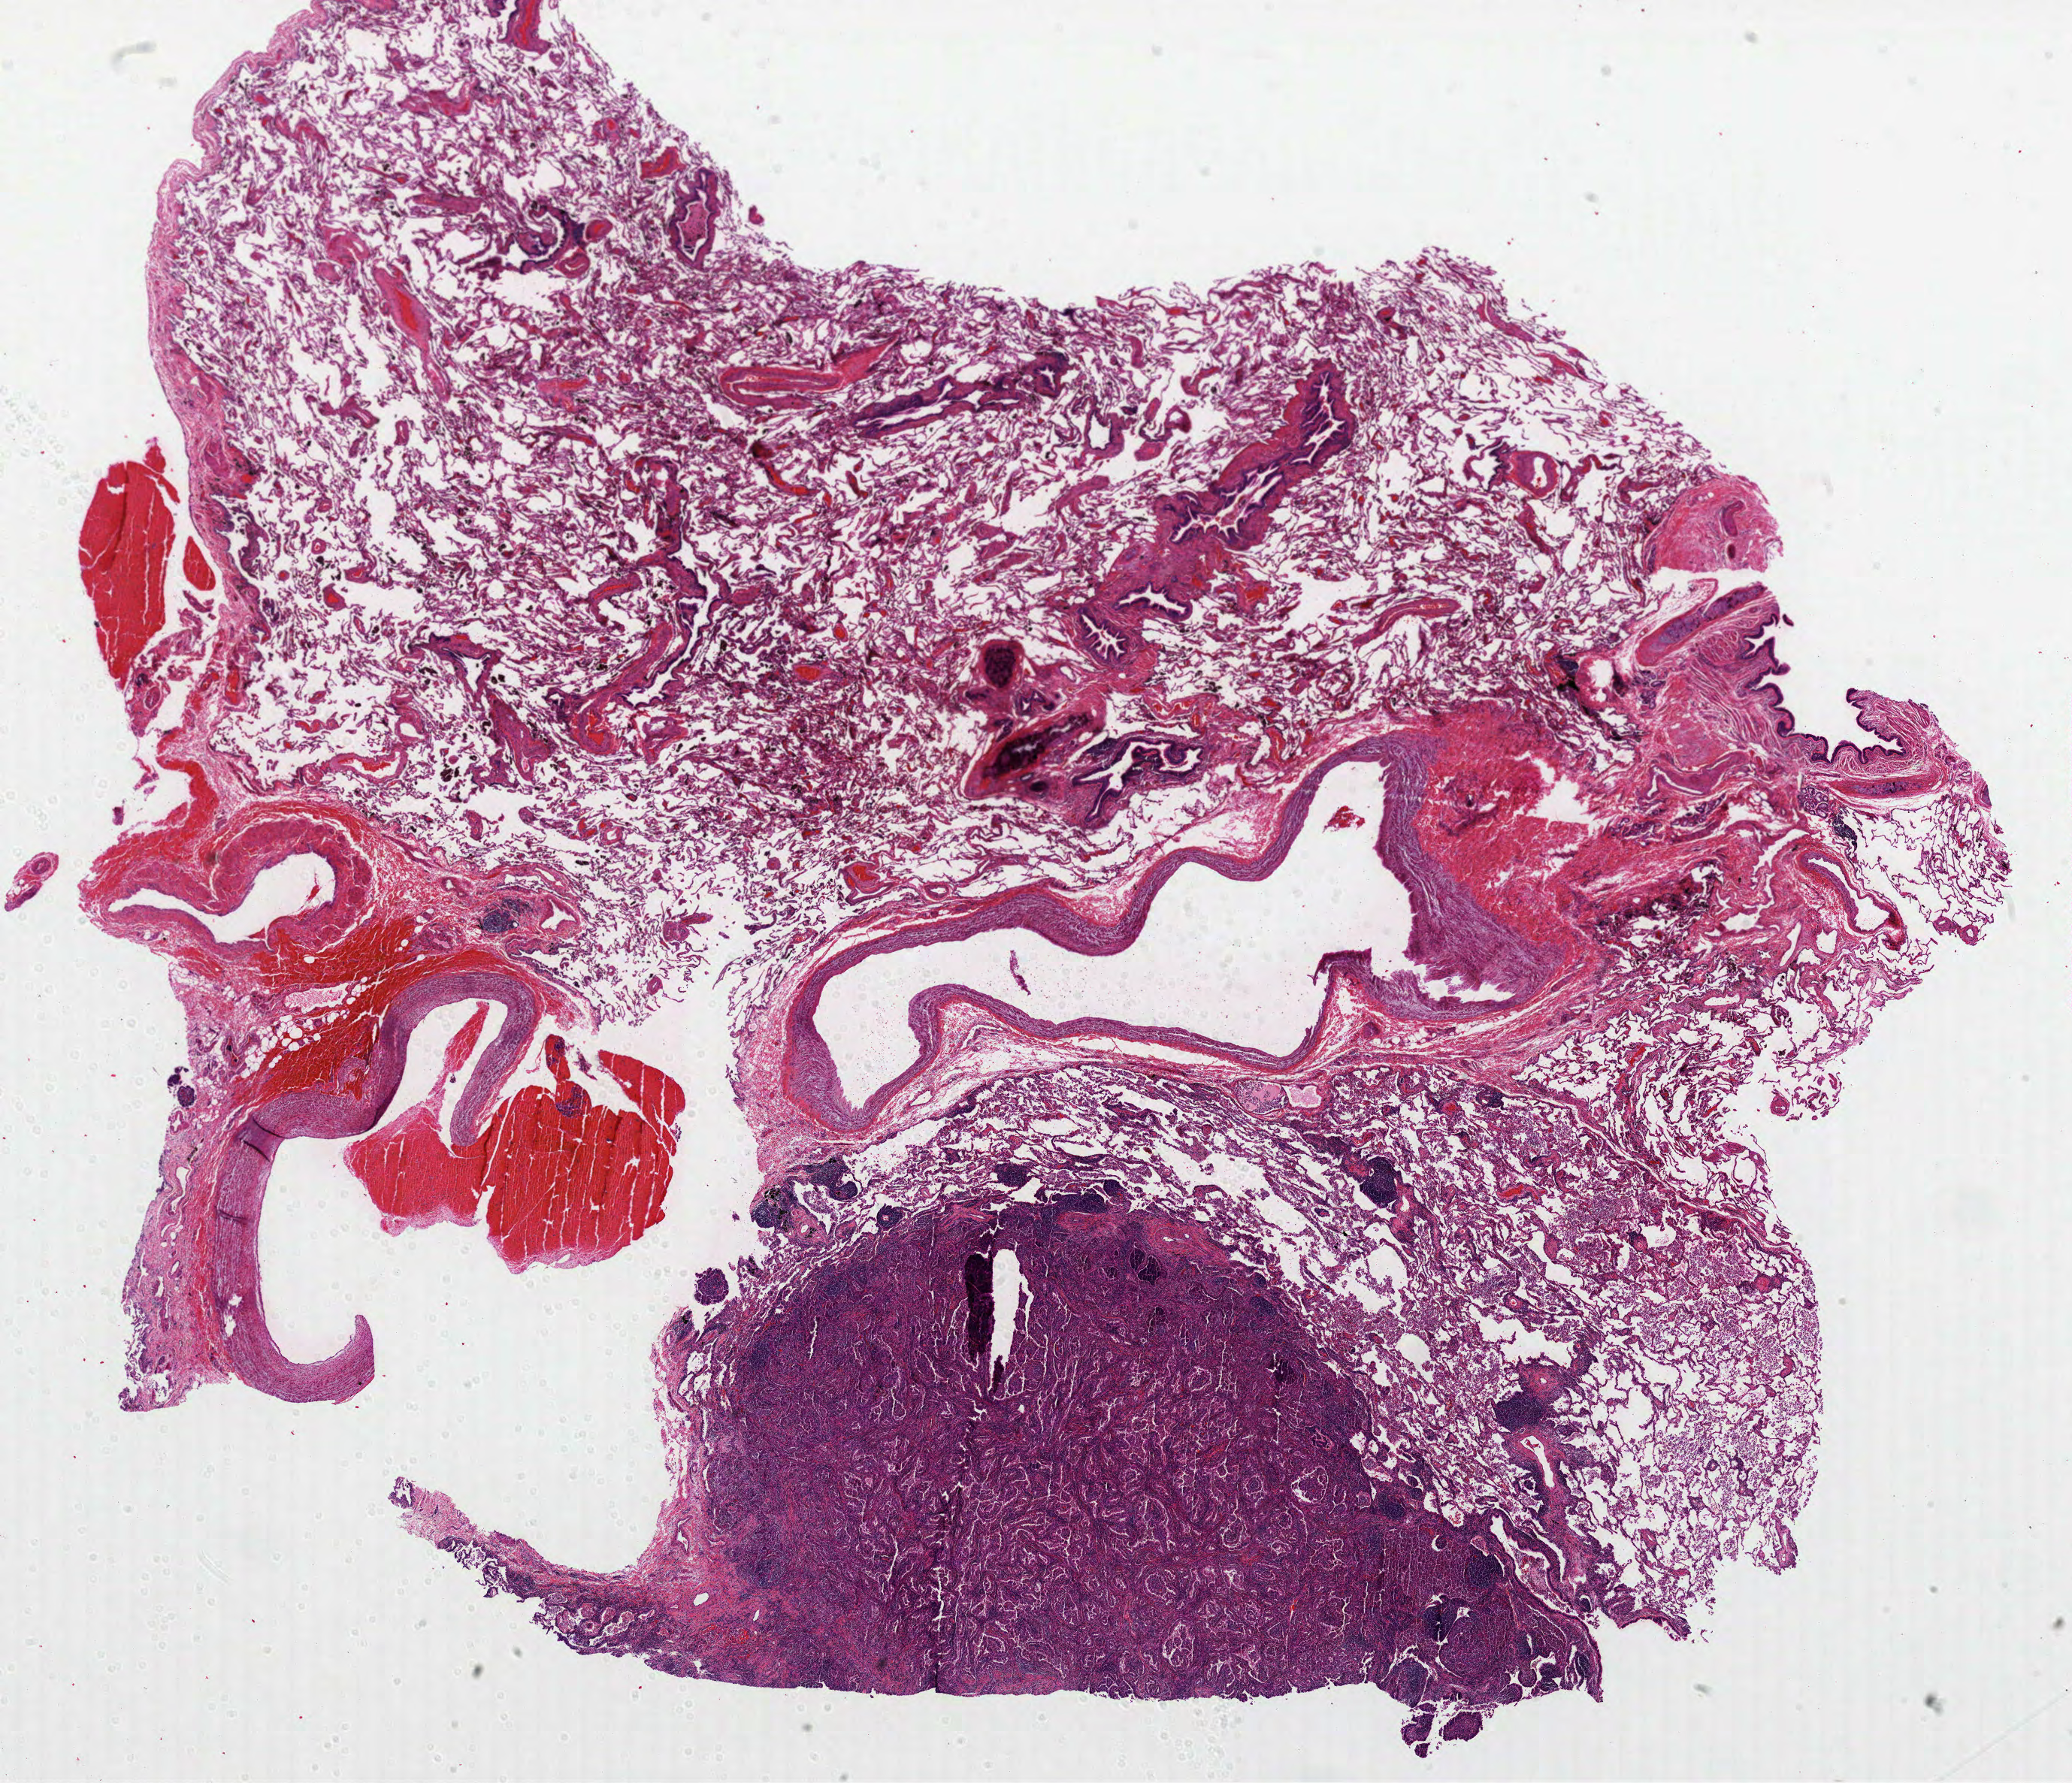
Whole-slide histology image, H&E, a low-resolution overview of the entire scanned area, about 22.2 x 19.1 mm. FFPE section. Lung, primary tumour sample. Female patient; age at initial diagnosis 79 years.
• AJCC pathologic stage: IA (6th edition)
• pathologic diagnosis: Papillary adenocarcinoma, NOS (upper lobe, lung)
• laterality: left